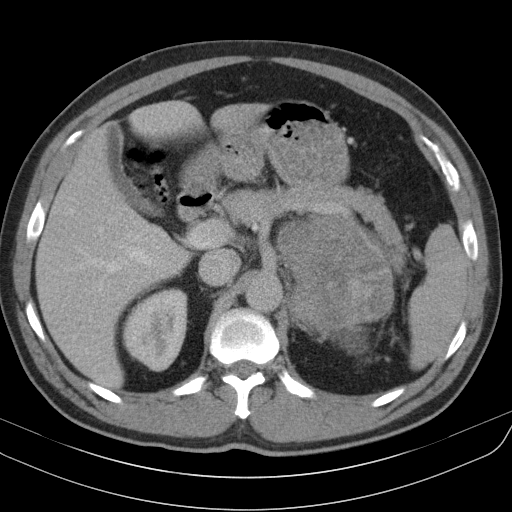
Contrast-enhanced abdominal CT, one axial slice; slice 69 of 91 in the series (ordered by position); reconstruction kernel B31s; 130 kVp; intravenous contrast given; soft-tissue window (W 400 / L 40 HU); 5 mm slice thickness; 512 × 512 image matrix. Male patient, age 51 years. Case-level facts recorded for this patient, not image findings: diagnosis: adrenocortical carcinoma; tumour side: left adrenal; tumour size at pathology: 18 cm; Ki-67 index: 40 %; stage (as recorded): 3.
Outlined on this slice (semi-automatic segmentation, software-assisted and operator-edited):
- mass: bounding box (x1, y1, x2, y2) in pixels: (281, 217, 392, 332)